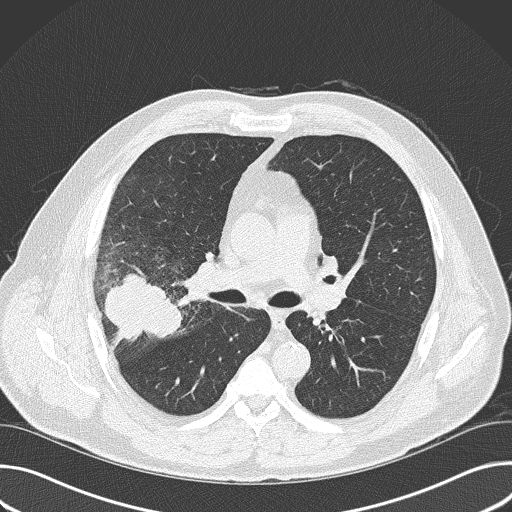
Axial slice from a low-dose chest CT screening exam, first (baseline) screen, lung window (W 1500 / L -600 HU), slice 98 of 157 in the series. Male participant, aged 56 years at enrolment.
Lesion marked by an expert reader, bounding box <80,259,184,363> (left, top, right, bottom; pixels). Screening reader's record for this exam (one nodule recorded; not confirmed to be the boxed lesion): non-calcified nodule or mass ≥4 mm, right upper lobe, 6 × 5 mm, spiculated (stellate) margins, soft tissue attenuation. Official screen result: positive, change unspecified: nodule(s) >= 4 mm or enlarging nodule(s), mass(es), or other non-specific abnormalities suspicious for lung cancer.